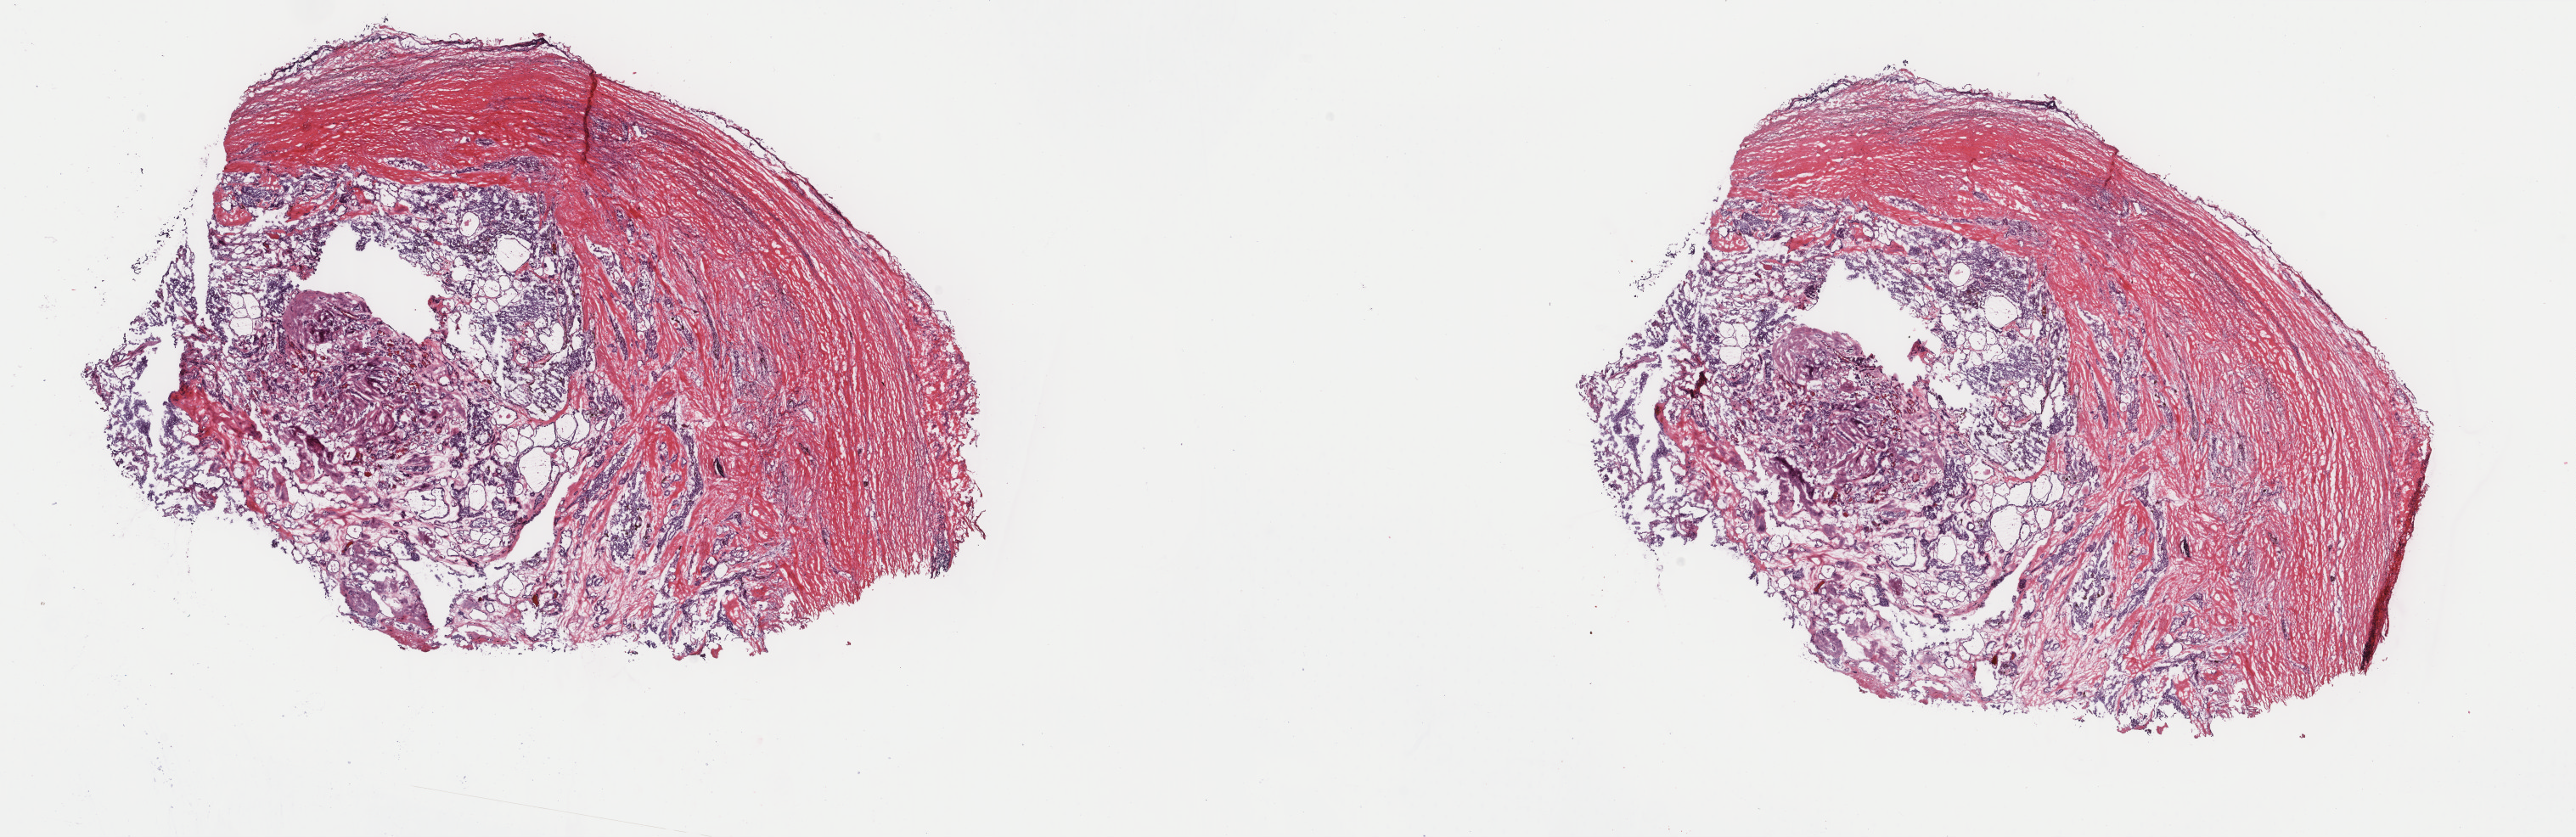
Digitized H&E tissue section (whole slide), whole scanned area (about 24.1 x 7.8 mm) shown as a low-resolution overview, frozen section from the top of the tissue portion, thyroid, primary tumour sample. Male patient; age at initial diagnosis 68 years. Slide review estimates, as recorded: tumour cells 45%, tumour nuclei 100%, normal cells 0%, stromal cells 55%, necrosis 0%. Infiltration values recorded for this section: lymphocyte infiltration 2%, monocyte infiltration 1%, neutrophil infiltration 0%.
TNM: T2 N0 M0. AJCC pathologic stage: II (7th edition). Histologic diagnosis: Papillary adenocarcinoma, NOS. Laterality: right.